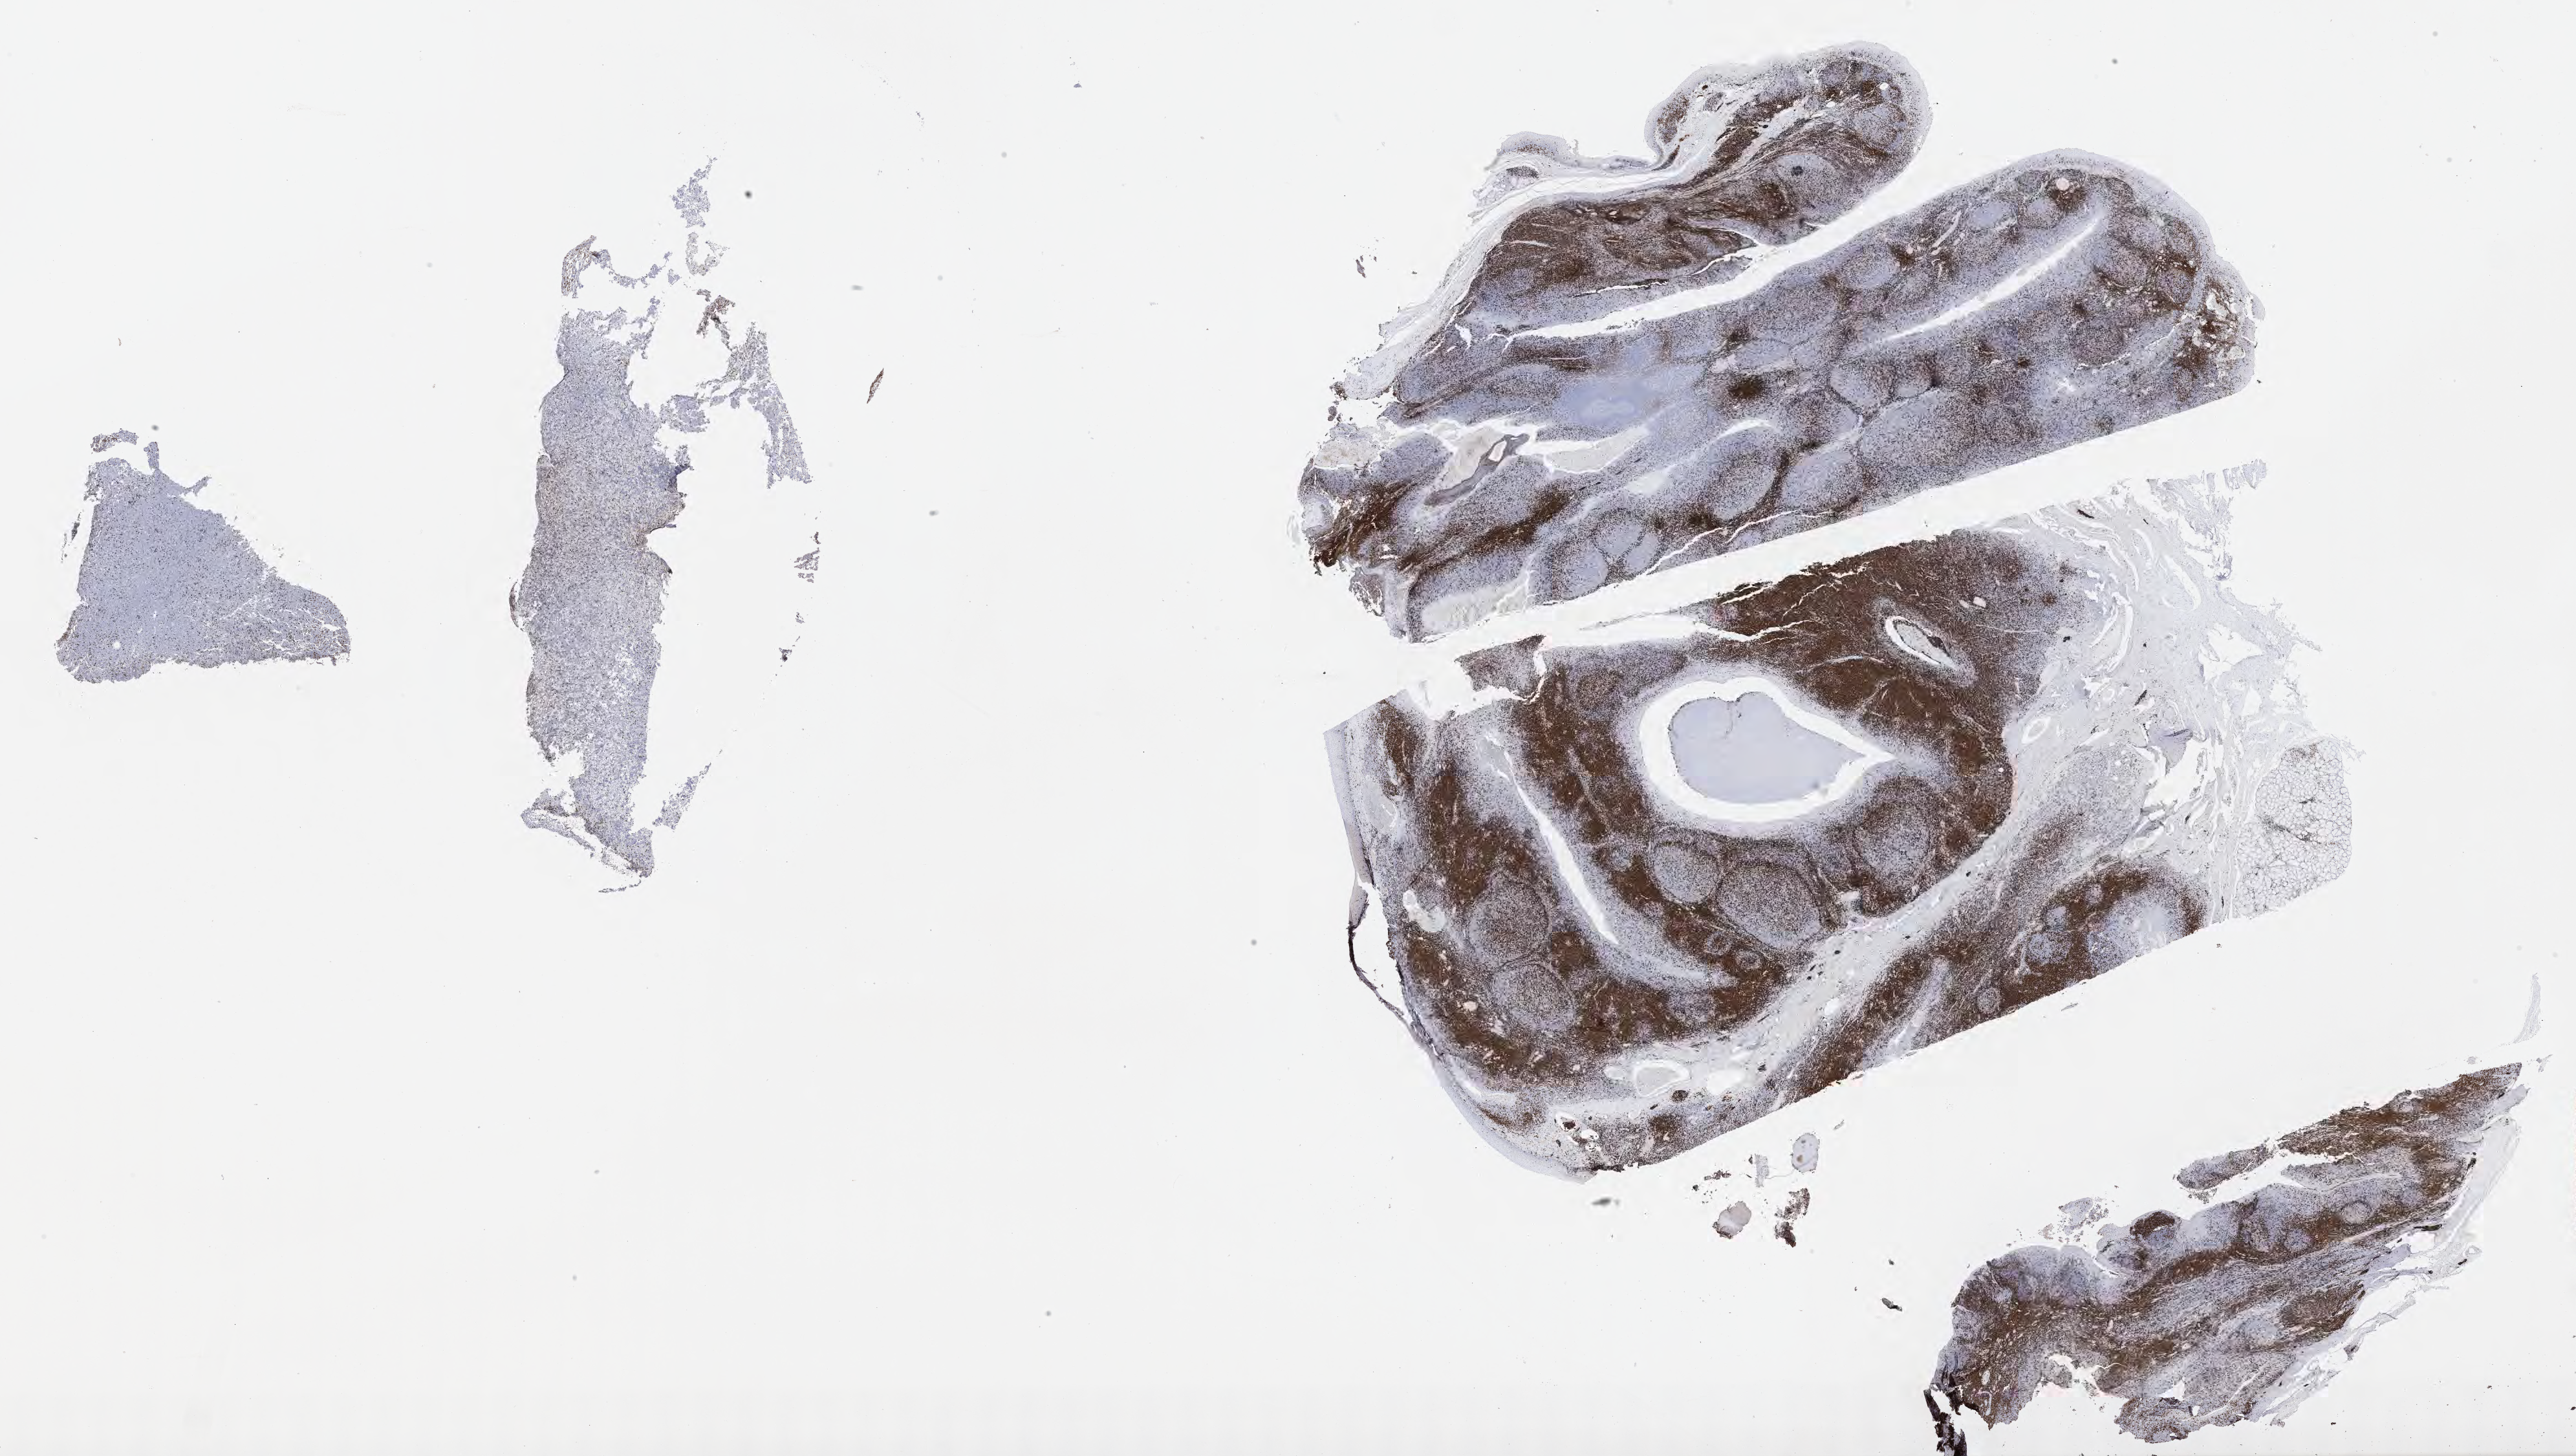
Whole-slide image, immunohistochemical stain for CD3, low-resolution overview of the scanned area, about 32.2 x 18.2 mm, tumor tissue. Male patient; age at initial diagnosis 2 years.
• diagnosis: Burkitt lymphoma, NOS